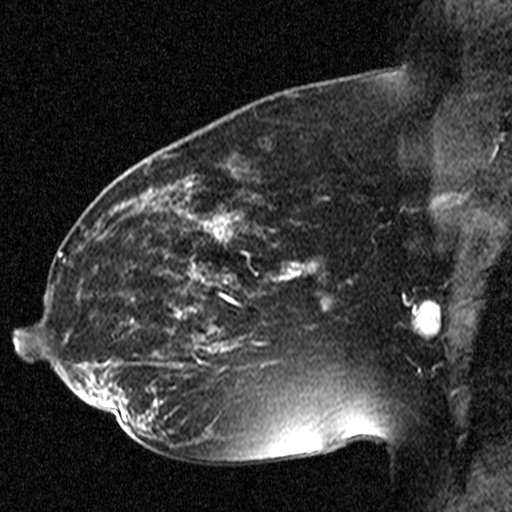
Breast MRI (dynamic contrast-enhanced), one sagittal slice; position 27 of 44 along the scan axis; dynamic contrast-enhanced study with each time point stored as its own series, time point 2 of 3 at this slice position (early post-contrast, ordered by acquisition time); 1.5 T; TE 4.5 ms, TR 11 ms; 512 × 512 image matrix, field of view 200 × 200 mm. Patient: female, 38 years. From the clinical record (not read from this slice): setting: breast cancer imaged before/during neoadjuvant chemotherapy; receptor status: HR-positive, HER2-negative.
Outlined on this slice (semi-automatic segmentation, software-assisted and operator-edited):
- analysis volume of interest (the breast-tissue region the enhancement analysis was run in; not a lesion): bounding box <176,272,251,349> (left, top, right, bottom; pixels)
- tumour enhancement mask (voxels above the 90 % enhancement threshold inside the analysis volume of interest): <182,272,240,345>